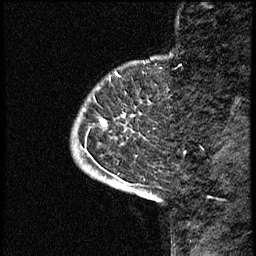
Breast MRI (dynamic contrast-enhanced), one sagittal slice; position 7 of 68 along the scan axis; dynamic contrast-enhanced study with each time point stored as its own series, time point 2 of 3 at this slice position (early post-contrast, ordered by acquisition time); 1.5 T; TE 4.2 ms, TR 17.6 ms; 256 × 256 image matrix, field of view 200 × 200 mm. Female patient, age 52 years. Case-level facts recorded for this patient, not image findings: setting: breast cancer imaged before/during neoadjuvant chemotherapy; receptor status: HER2-positive.
Structures marked on this image (semi-automatic segmentation, software-assisted and operator-edited):
- analysis volume of interest (the breast-tissue region the enhancement analysis was run in; not a lesion): bounding box <71,61,170,184> (left, top, right, bottom; pixels)
- tumour enhancement mask (voxels above the 100 % enhancement threshold inside the analysis volume of interest): <113,179,120,184>